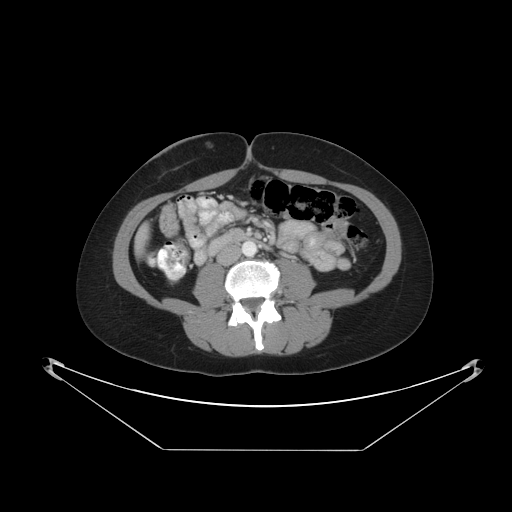
Contrast-enhanced abdominal CT, one axial slice. Position 9 of 48 along the scan axis. Reconstruction kernel STANDARD. 120 kVp. Intravenous contrast given. Soft-tissue window (W 400 / L 40 HU). 512 × 512 image matrix, field of view 482 × 482 mm. Female patient, age 38 years. Case-level facts recorded for this patient, not image findings: diagnosis: colorectal cancer liver metastases, imaged before liver resection; multiple liver metastases: yes; largest metastasis: 2.5 cm; chemotherapy before resection: no.
Annotated regions visible in this slice (expert manual segmentation):
- liver: box from (x=138, y=229) to (x=146, y=257) px